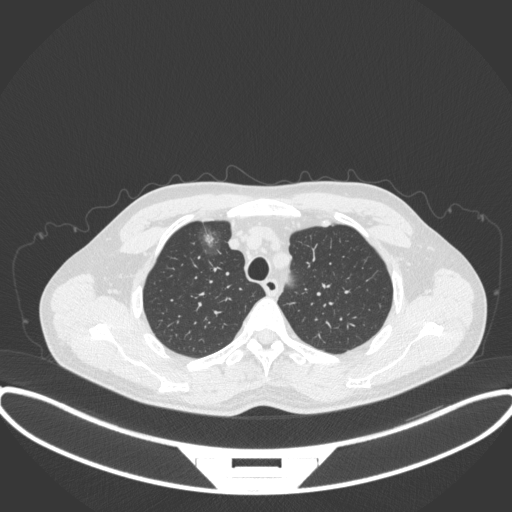
Chest CT, one axial slice; position 294 of 395 along the scan axis; reconstruction kernel B31f; lung window (W 1500 / L -600 HU); 512 × 512 image matrix, field of view 424 × 424 mm. Patient: male, 60 years. Case-level facts recorded for this patient, not image findings: clinical TNM (as recorded): T1c N0 M0.
Structures marked on this image (rectangle marked by the reading radiologist):
- lung tumour (recorded histology: adenocarcinoma): bounding box <198,225,222,265> (left, top, right, bottom; pixels)